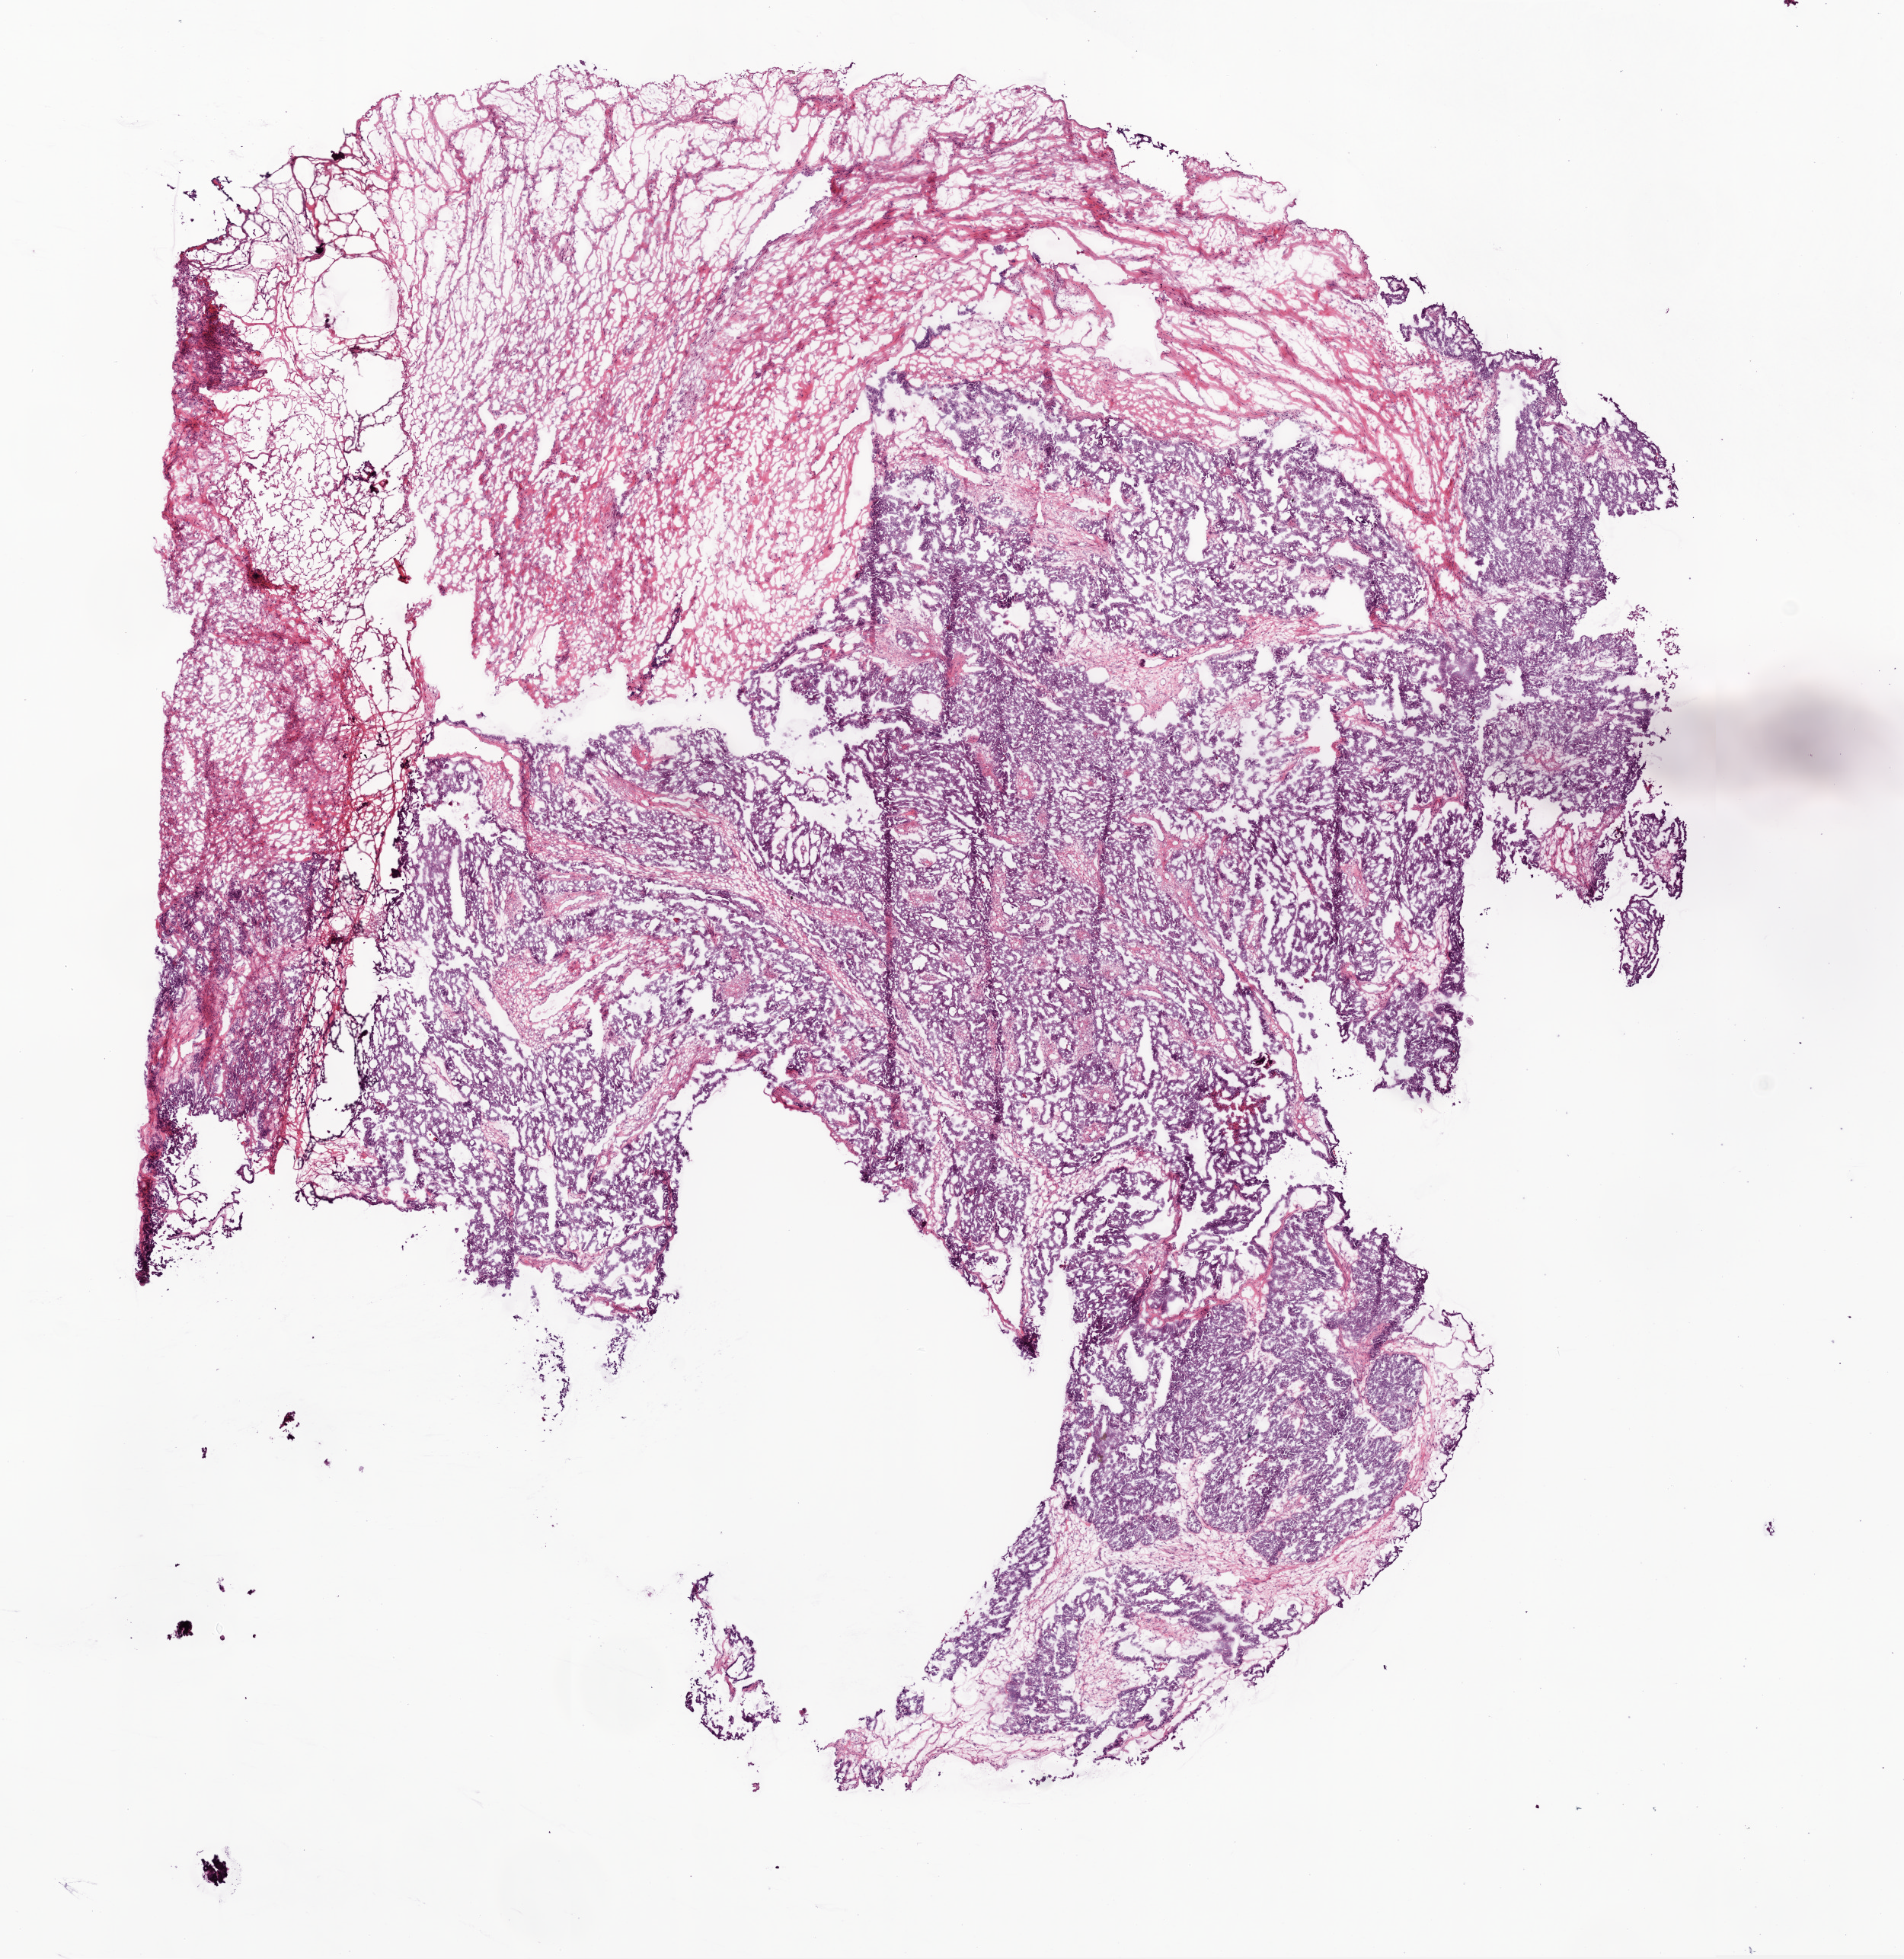
Digitized H&E tissue section (whole slide), shown as a low-resolution overview of the whole scanned area (about 10.0 x 10.3 mm, acquisition: 20x scan). Frozen section. Ovary, primary tumour sample. Female patient; age at initial diagnosis 68 years. Histologic grade: G3 (poorly differentiated). Composition of this section per pathologist review: tumour cells 60%, tumour nuclei 85%, normal cells 0%, stromal cells 38%, necrosis 2%.
Pathologic diagnosis: Serous cystadenocarcinoma, NOS. Laterality: bilateral. FIGO stage: IV.